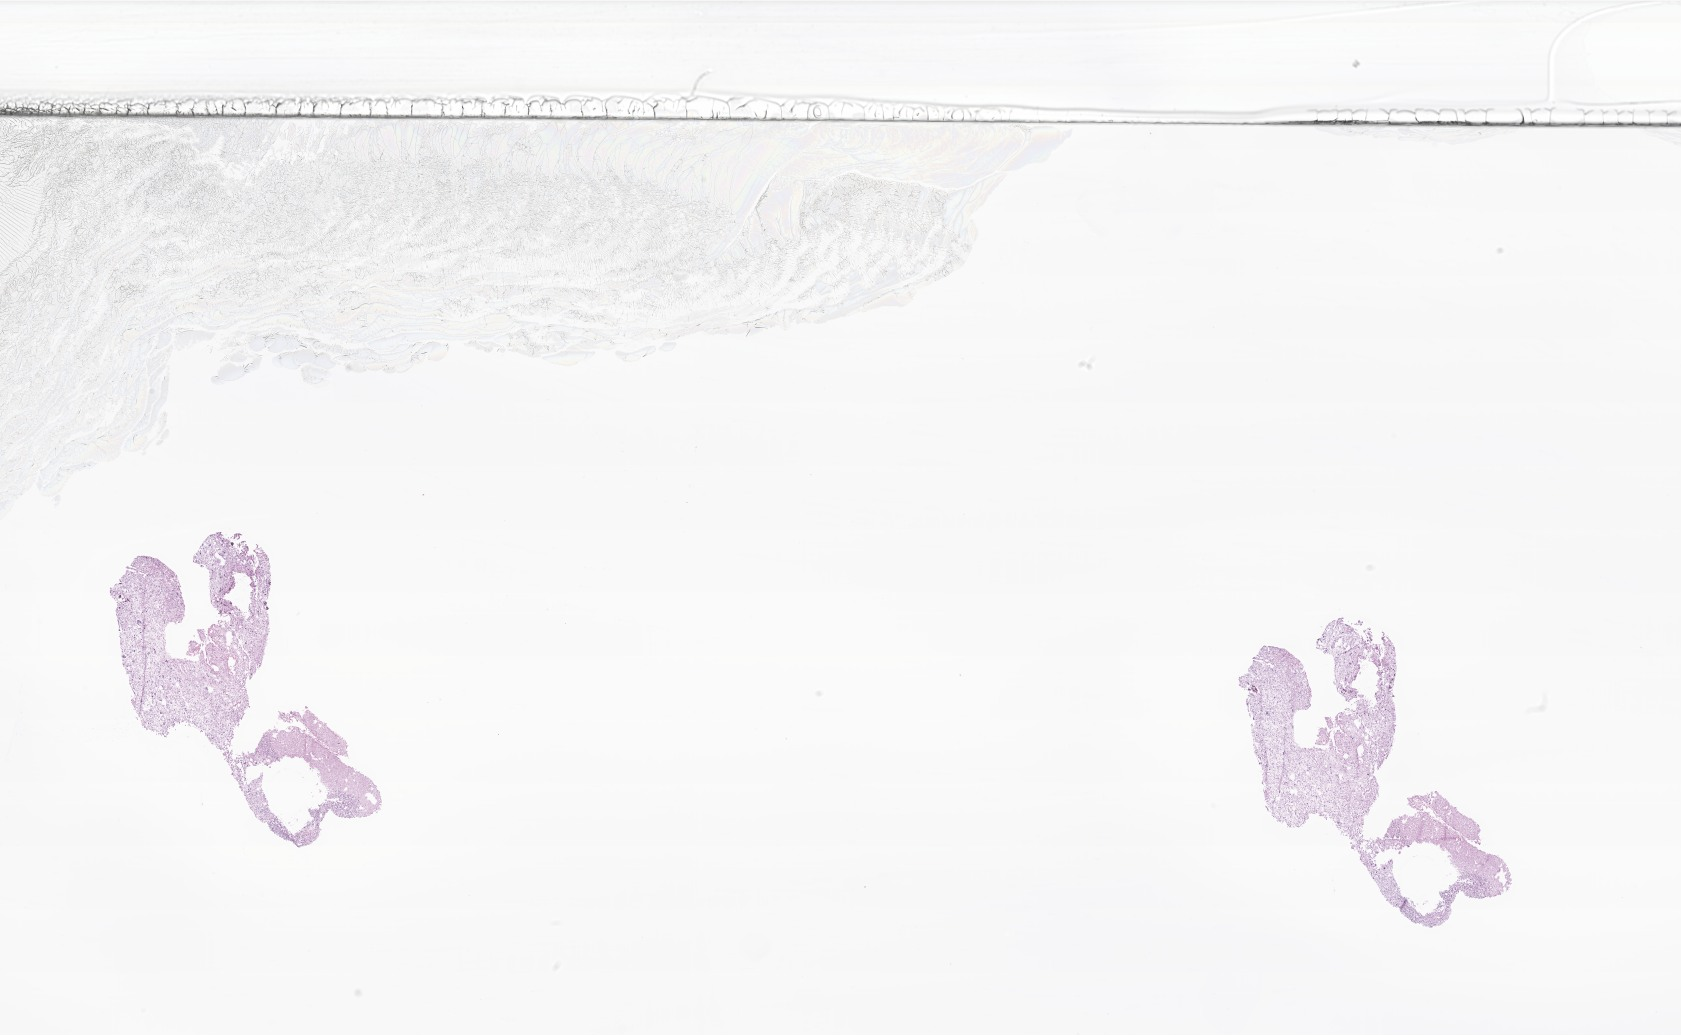
H&E whole-slide image of tumor tissue from the cerebellum, a low-resolution overview of the entire scanned area, about 28.4 x 17.5 mm; frozen section. Male patient, age 119 months.
• diagnosis: Glioma, malignant